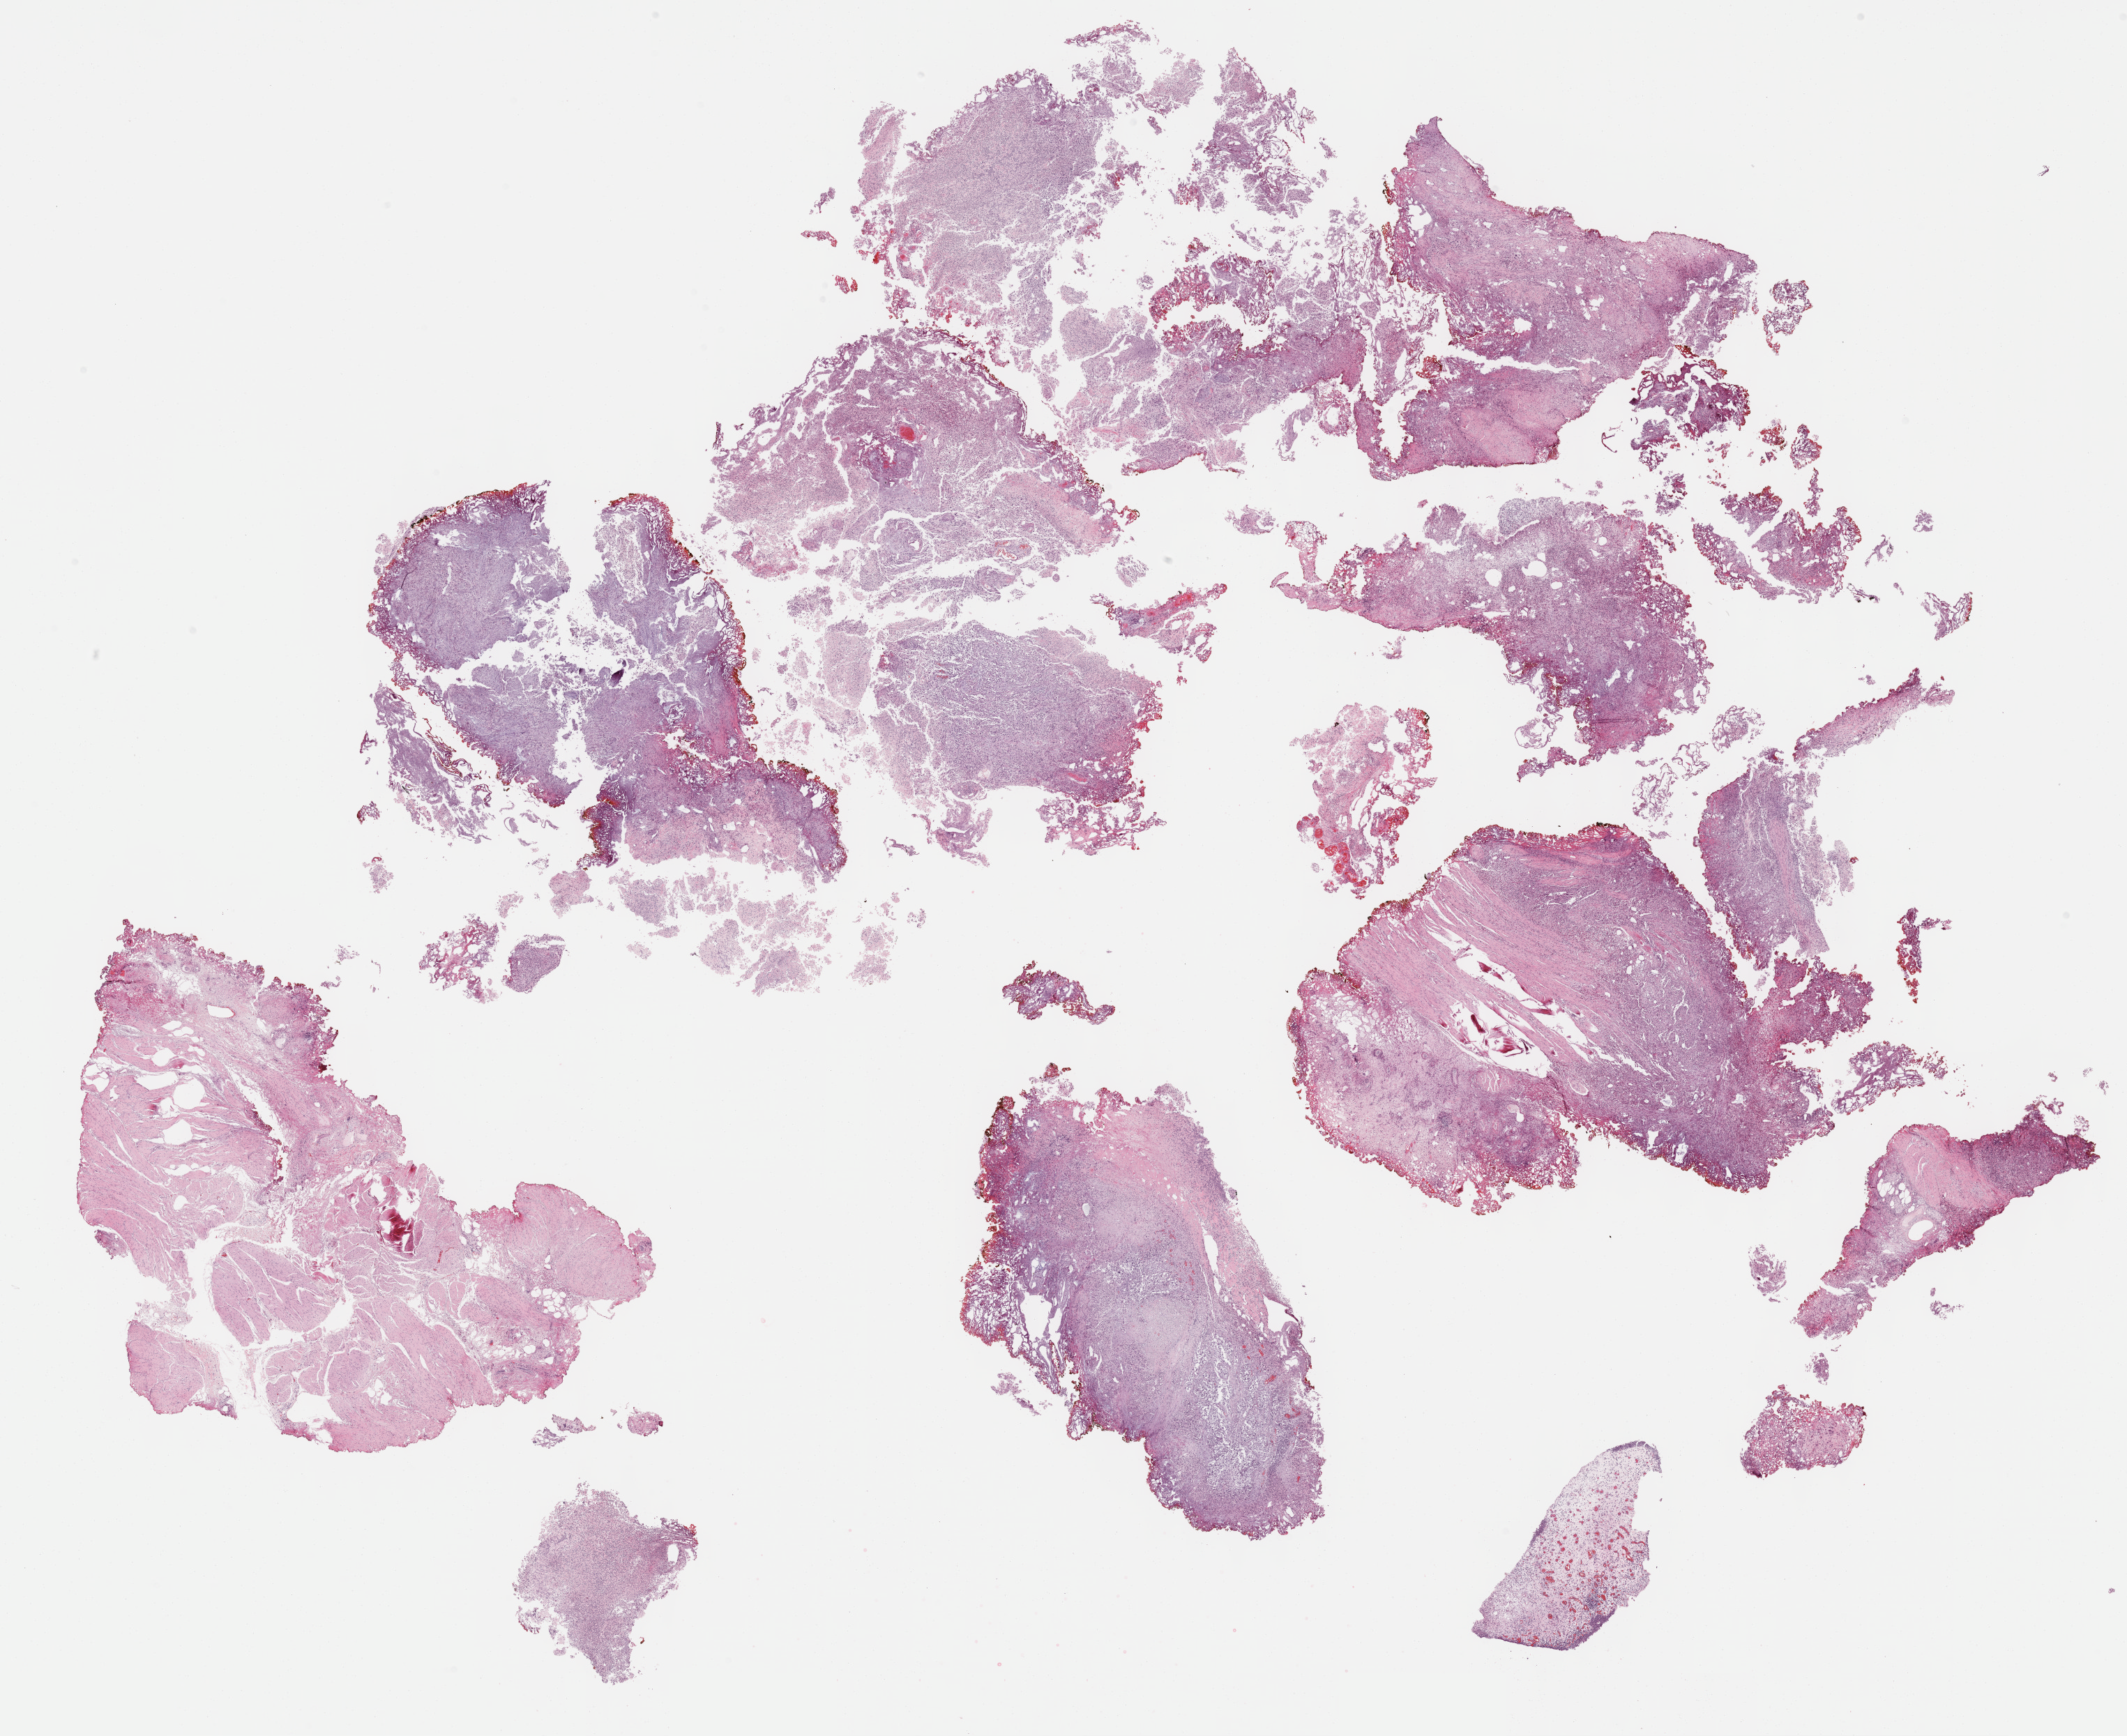
Digitized Hematoxylin and eosin (H&E) stained tissue section (whole slide), whole scanned area (about 24.7 x 20.1 mm) shown as a low-resolution overview. Formalin-fixed paraffin-embedded (FFPE) diagnostic section. Sample: primary tumour, bladder. Female patient; age at initial diagnosis 67 years. Histologic grade: high grade.
* AJCC pathologic stage: III
* lymph nodes positive (case pathology): 0 of 2 examined
* TNM: T3 N0 M0
* diagnosis: Transitional cell carcinoma (lateral wall of bladder)